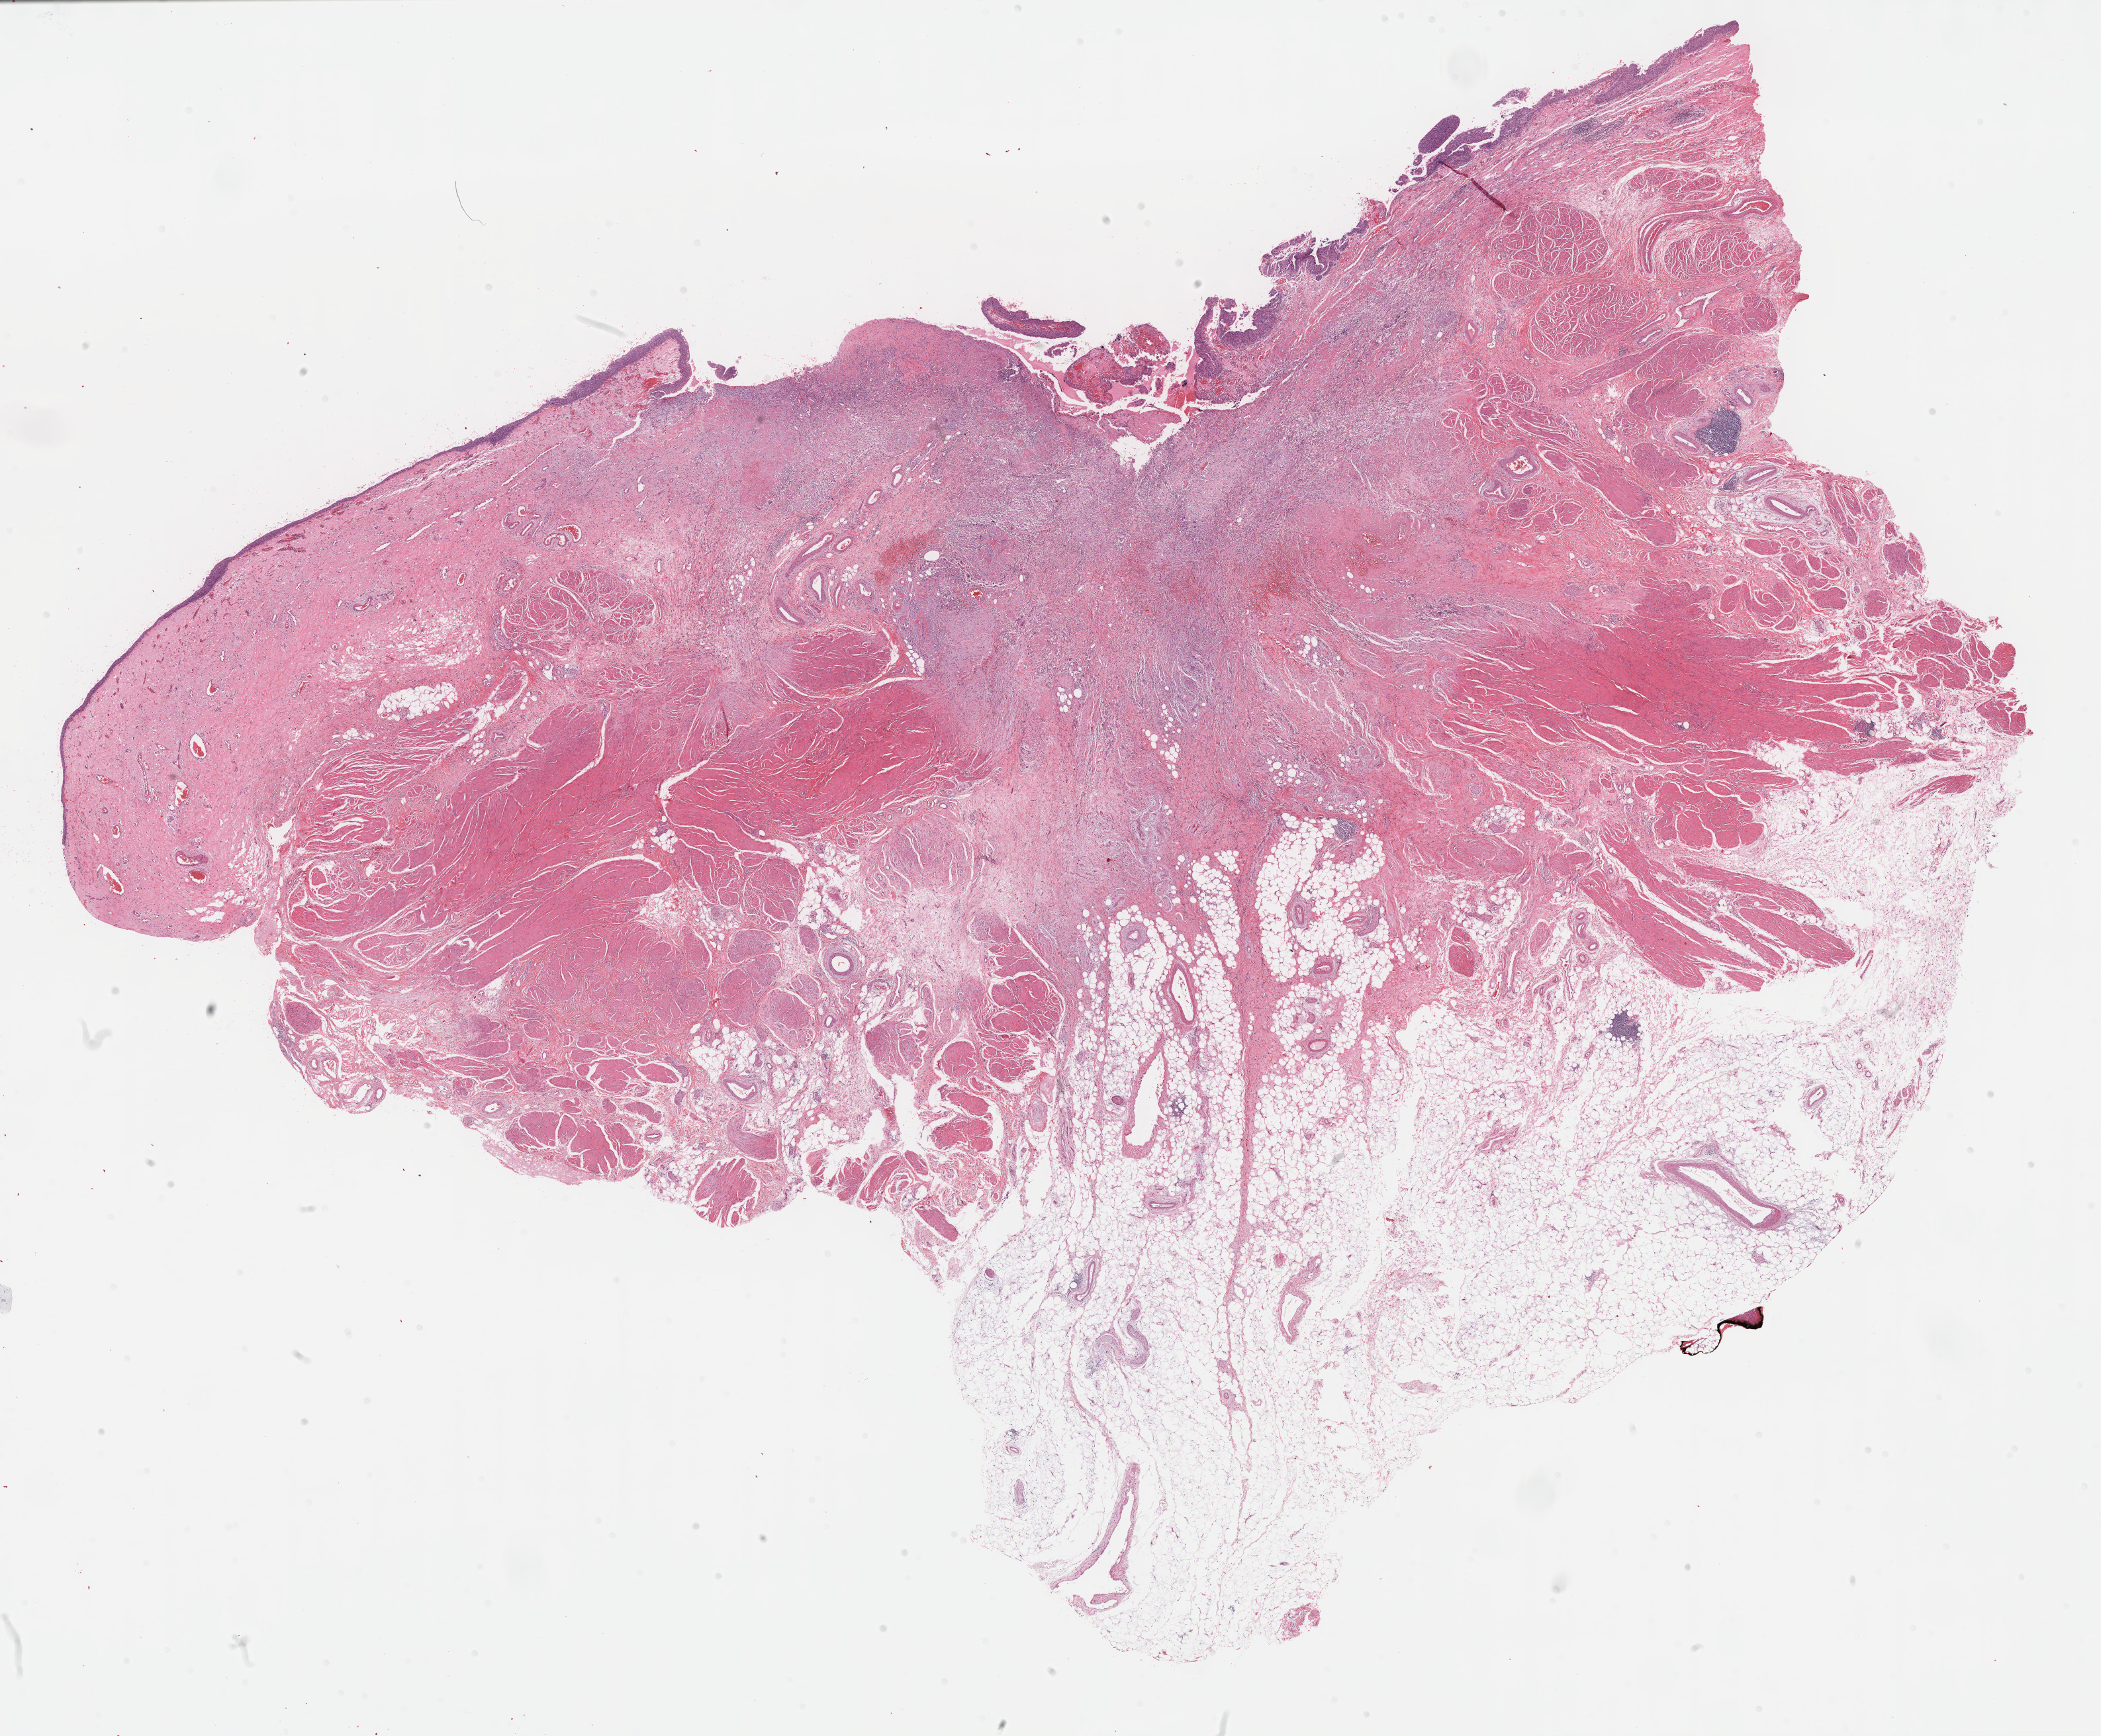
Digitized Hematoxylin and eosin (H&E) stained tissue section (whole slide) — low-resolution overview of the scanned area, about 25.7 x 21.2 mm; formalin-fixed paraffin-embedded (FFPE) diagnostic section; primary tumour sample from the bladder. Female, age 64 years at initial diagnosis.
Histologic diagnosis: Transitional cell carcinoma.